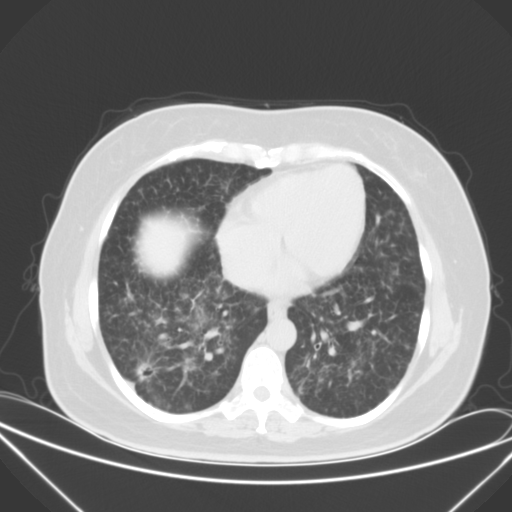
Chest CT, one axial slice. Position 18 of 52 along the scan axis. Lung window (W 1500 / L -600 HU). 5 mm slice thickness. 512 × 512 image matrix, field of view 386 × 386 mm. Patient: female, 50 years. From the clinical record (not read from this slice): clinical TNM (as recorded): T1c N0 M1a.
Outlined on this slice (rectangle marked by the reading radiologist):
- lung tumour (recorded histology: adenocarcinoma): bounding box [x1, y1, x2, y2] px = [129, 357, 163, 393]